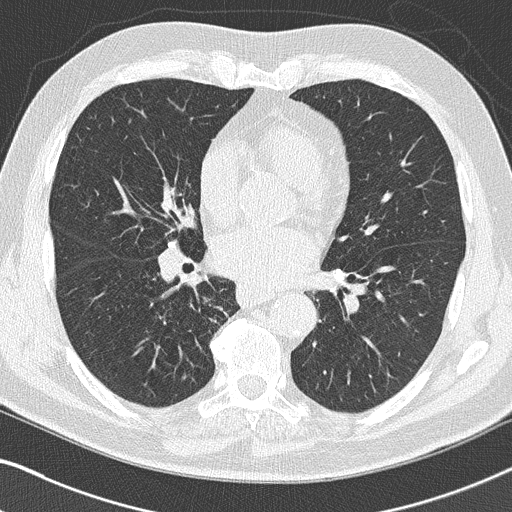
Axial slice from a low-dose chest CT screening exam. Third annual screen. Lung window (W 1500 / L -600 HU). Male participant, aged 66 years at enrolment.
Lesion marked by an expert reader, box from (x=141, y=260) to (x=232, y=324) px. Reader record for this screening exam (exam-level; its link to the box is not recorded): non-calcified nodule or mass ≥4 mm, right upper lobe, 5 × 4 mm, smooth margins, pre-existing on the prior screen: yes; interval growth: no. Official screen result: positive, other.